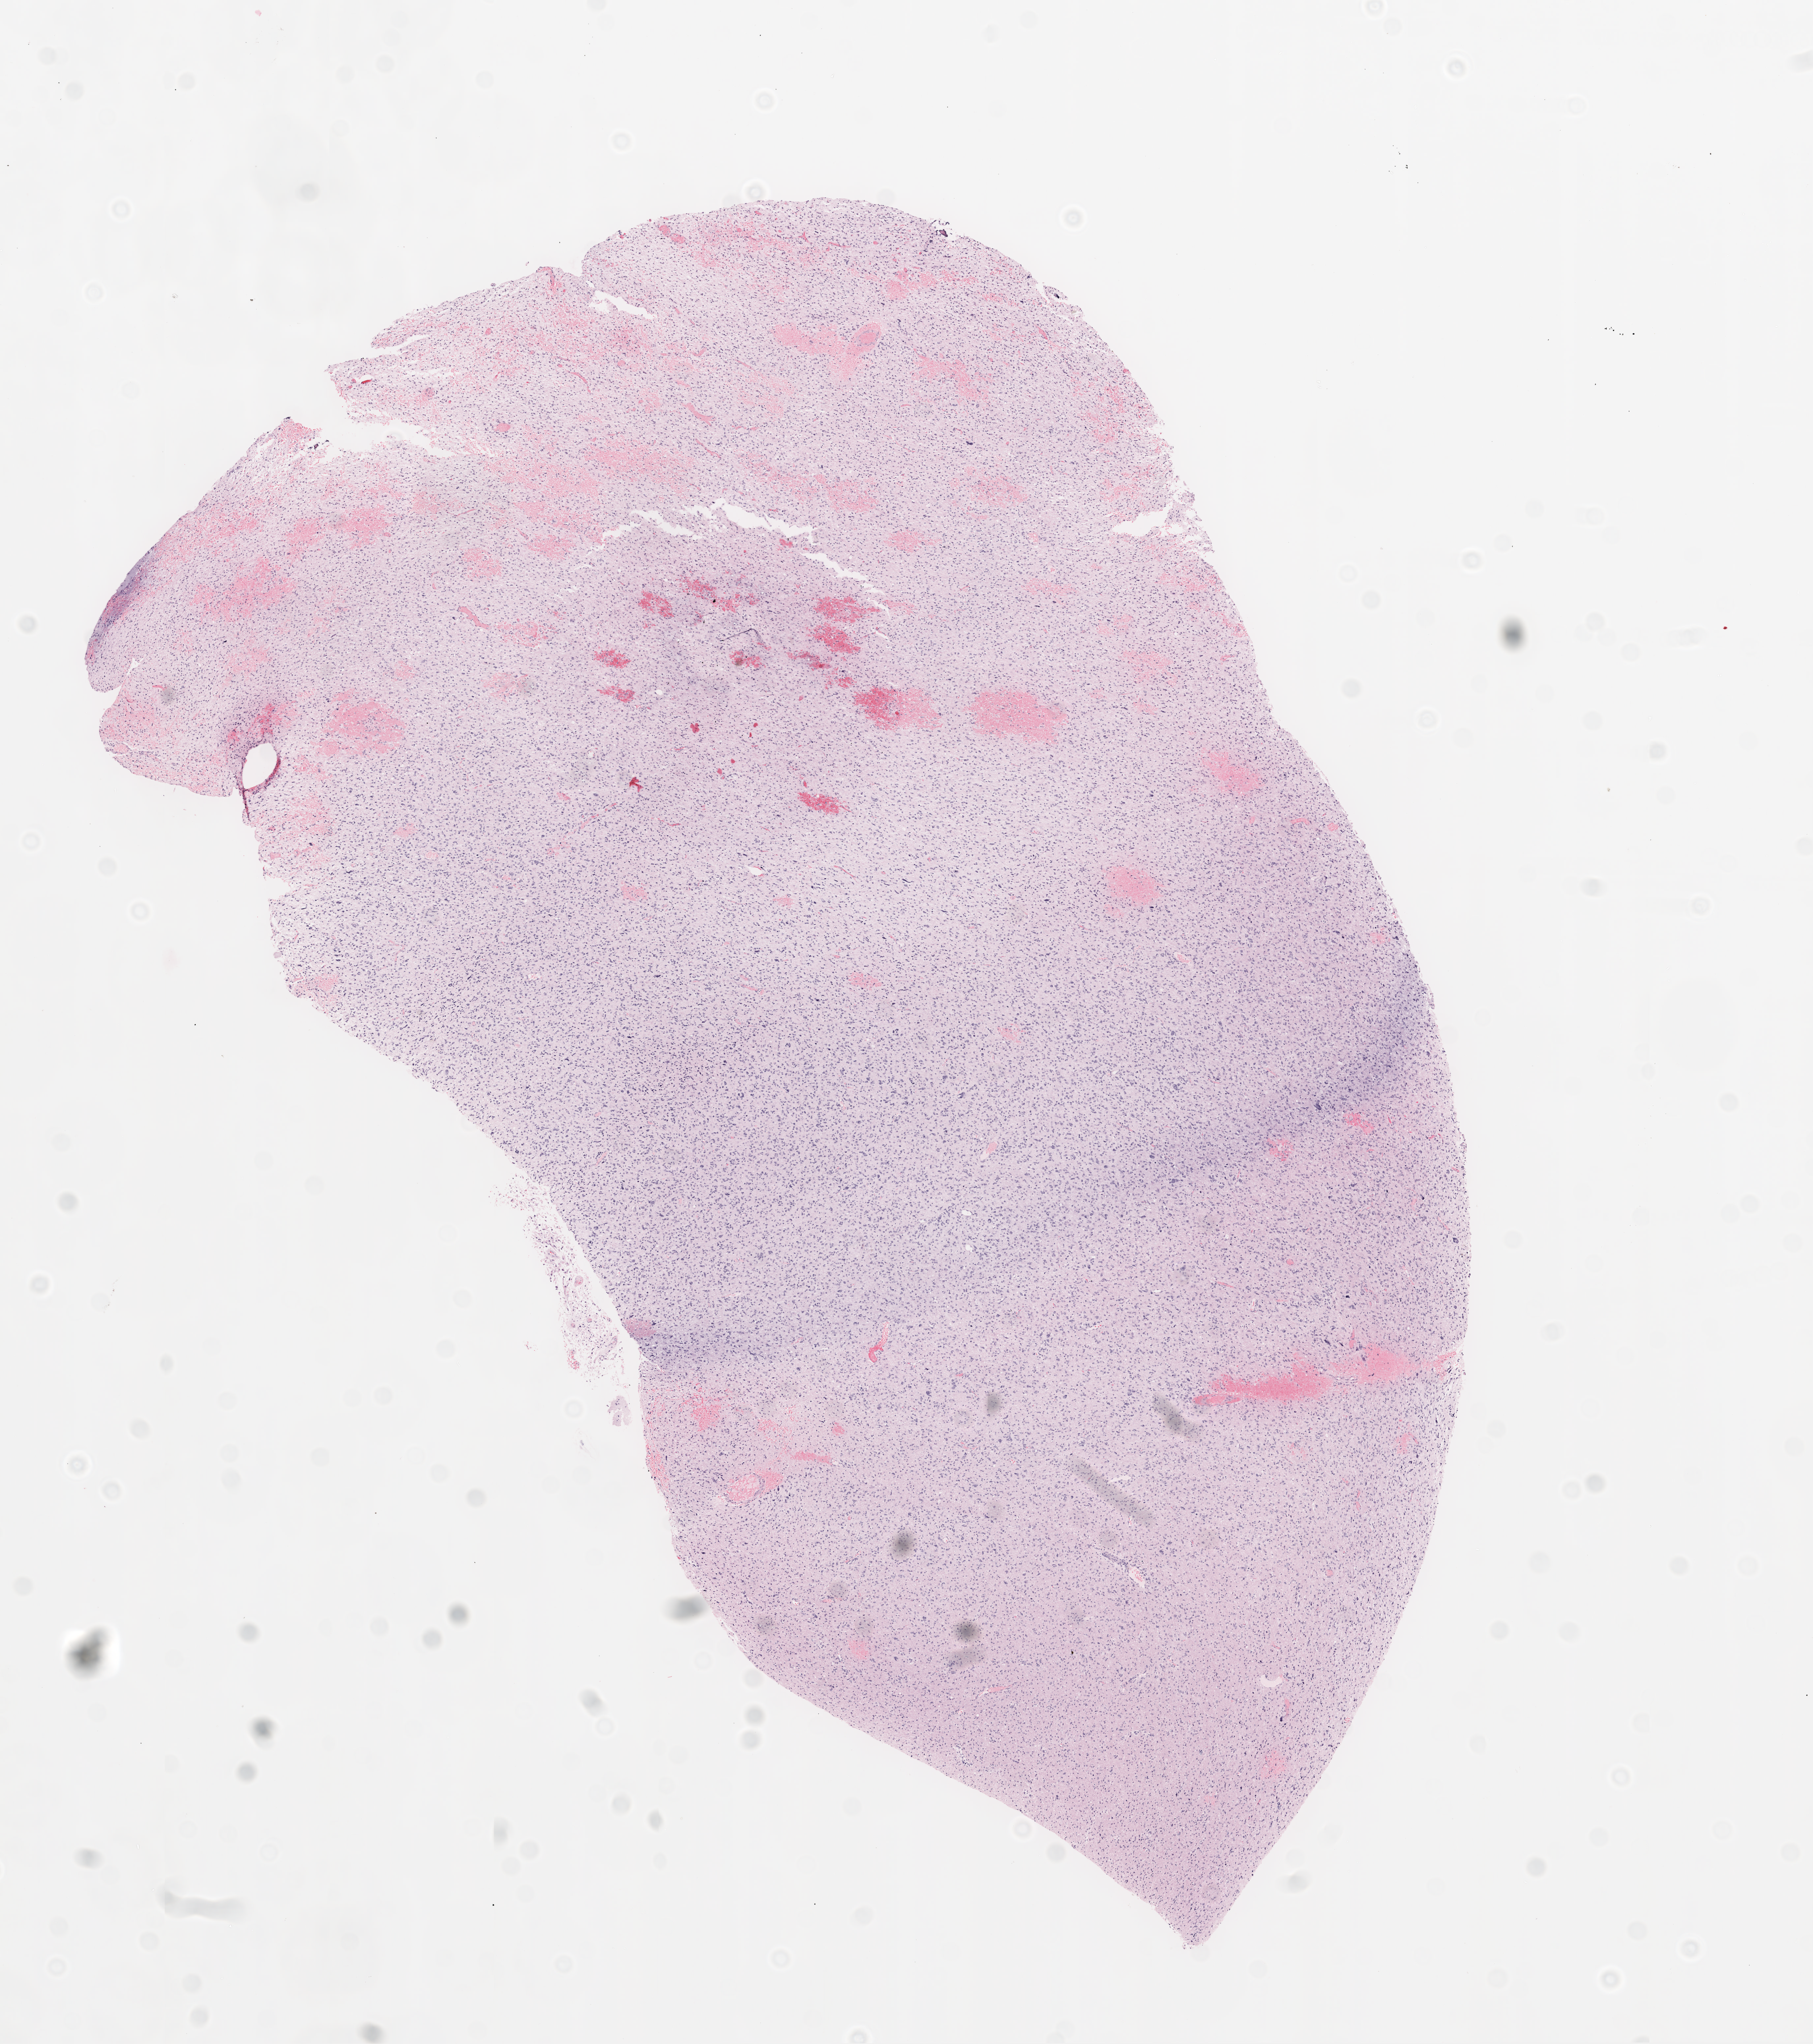
Whole-slide histology image, Hematoxylin and eosin (H&E) stained, a low-resolution overview of the entire scanned area, about 11.0 x 12.4 mm (acquisition: 20x scan); frozen section; primary tumour sample from the brain. Patient: female, age at initial diagnosis 76 years. Composition of this section per pathologist review: tumour cells 100%, tumour nuclei 85%, normal cells 0%, stromal cells 0%, necrosis 0%.
• diagnosis: Glioblastoma